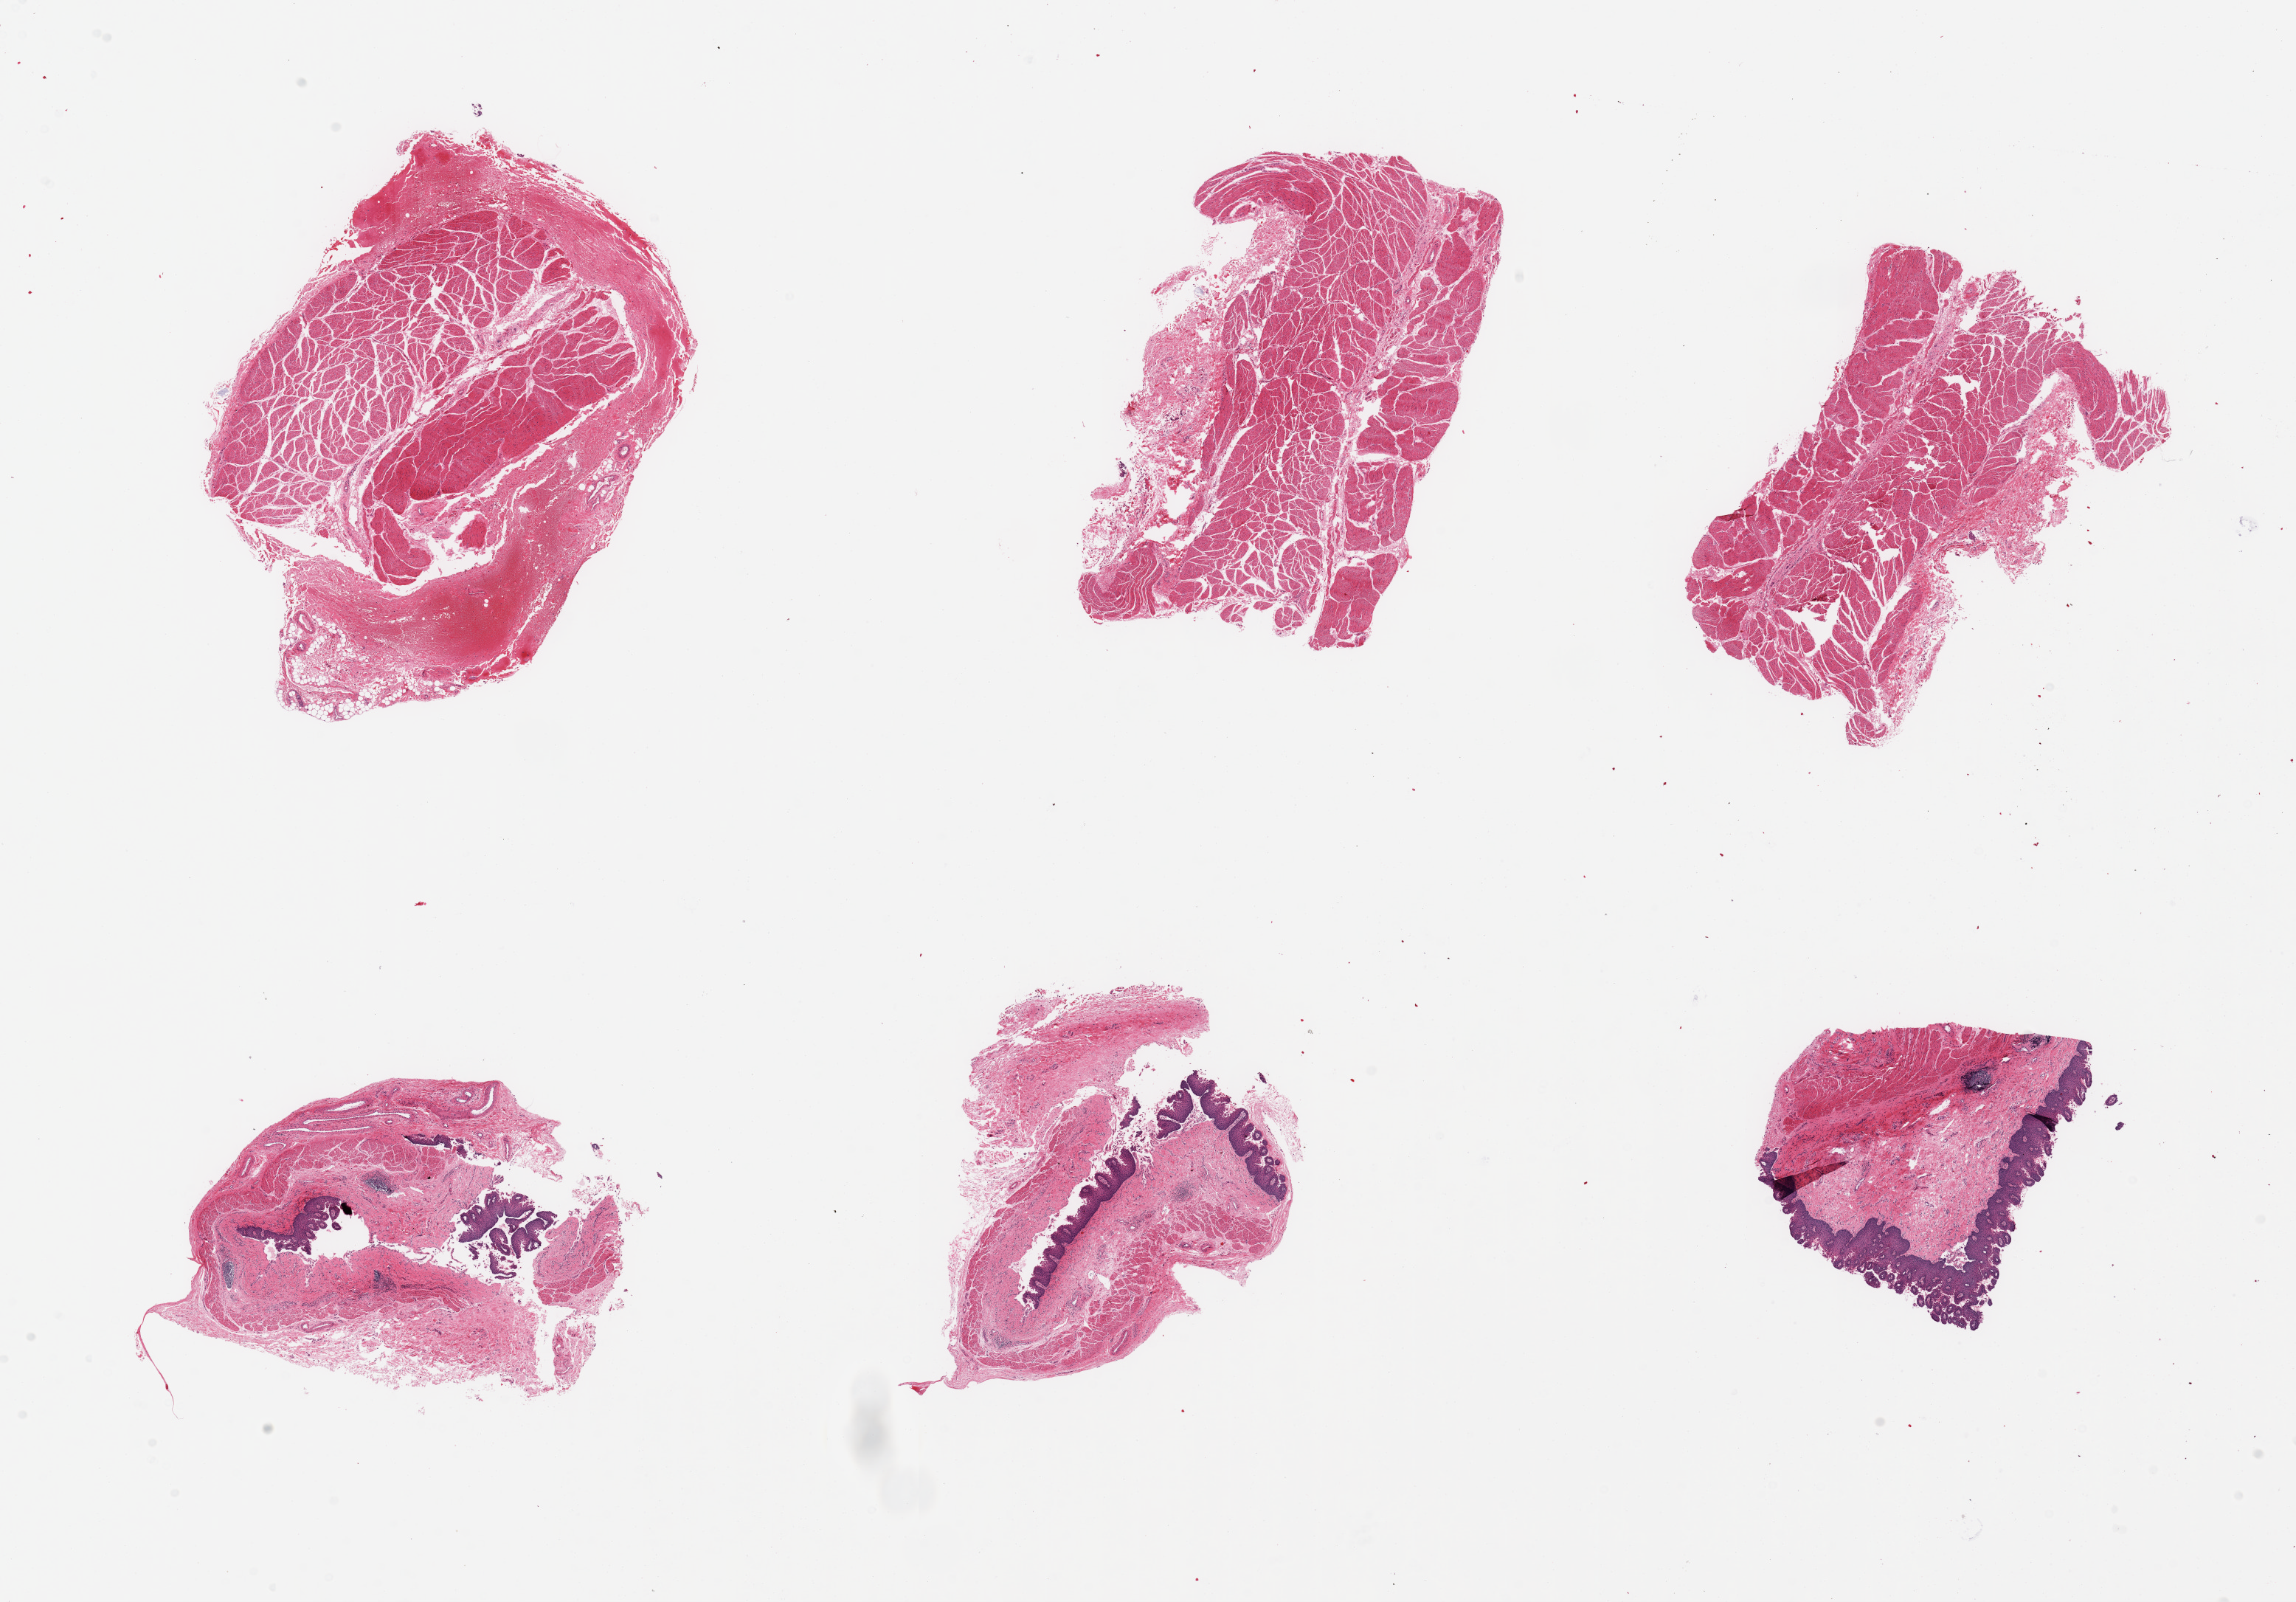
Whole-slide image, haematoxylin and eosin stain, brightfield — low-resolution overview of the scanned area, about 24.6 x 17.2 mm (slide scanned at 20x); PAXgene-fixed paraffin-embedded (PFPE) section; target tissue: esophageal mucous membrane; donor tissue sample. Donor: male.
* review note (as recorded): 6 pieces; 3 are muscularis, 3 are mucosa